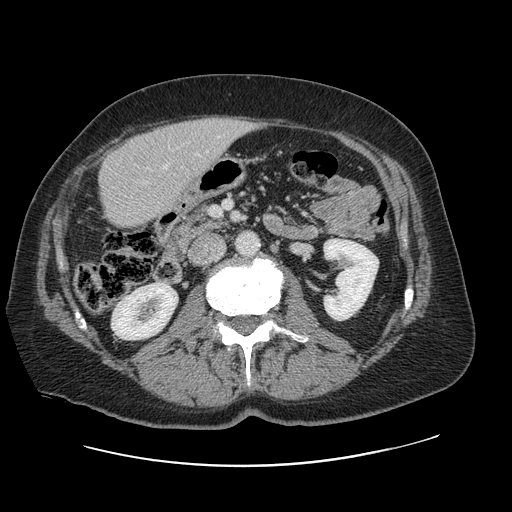
Contrast-enhanced abdominal CT, one axial slice; position 29 of 138 along the scan axis; 120 kVp; soft-tissue window (W 400 / L 40 HU); 2.5 mm slice thickness; 512 × 512 image matrix, field of view 402 × 402 mm. Male patient, age 71 years. From the clinical record (not read from this slice): diagnosis: colorectal cancer liver metastases, imaged before liver resection; multiple liver metastases: no; largest metastasis: 3.3 cm; disease in both lobes: no.
Annotated regions visible in this slice (outlined manually by an expert reader):
- liver: bounding box (x1, y1, x2, y2) in pixels: (100, 118, 254, 227)
- planned liver remnant (the part of the liver to remain after resection): (100, 133, 182, 226)
- portal vein (with intrahepatic branches): (164, 166, 167, 169)